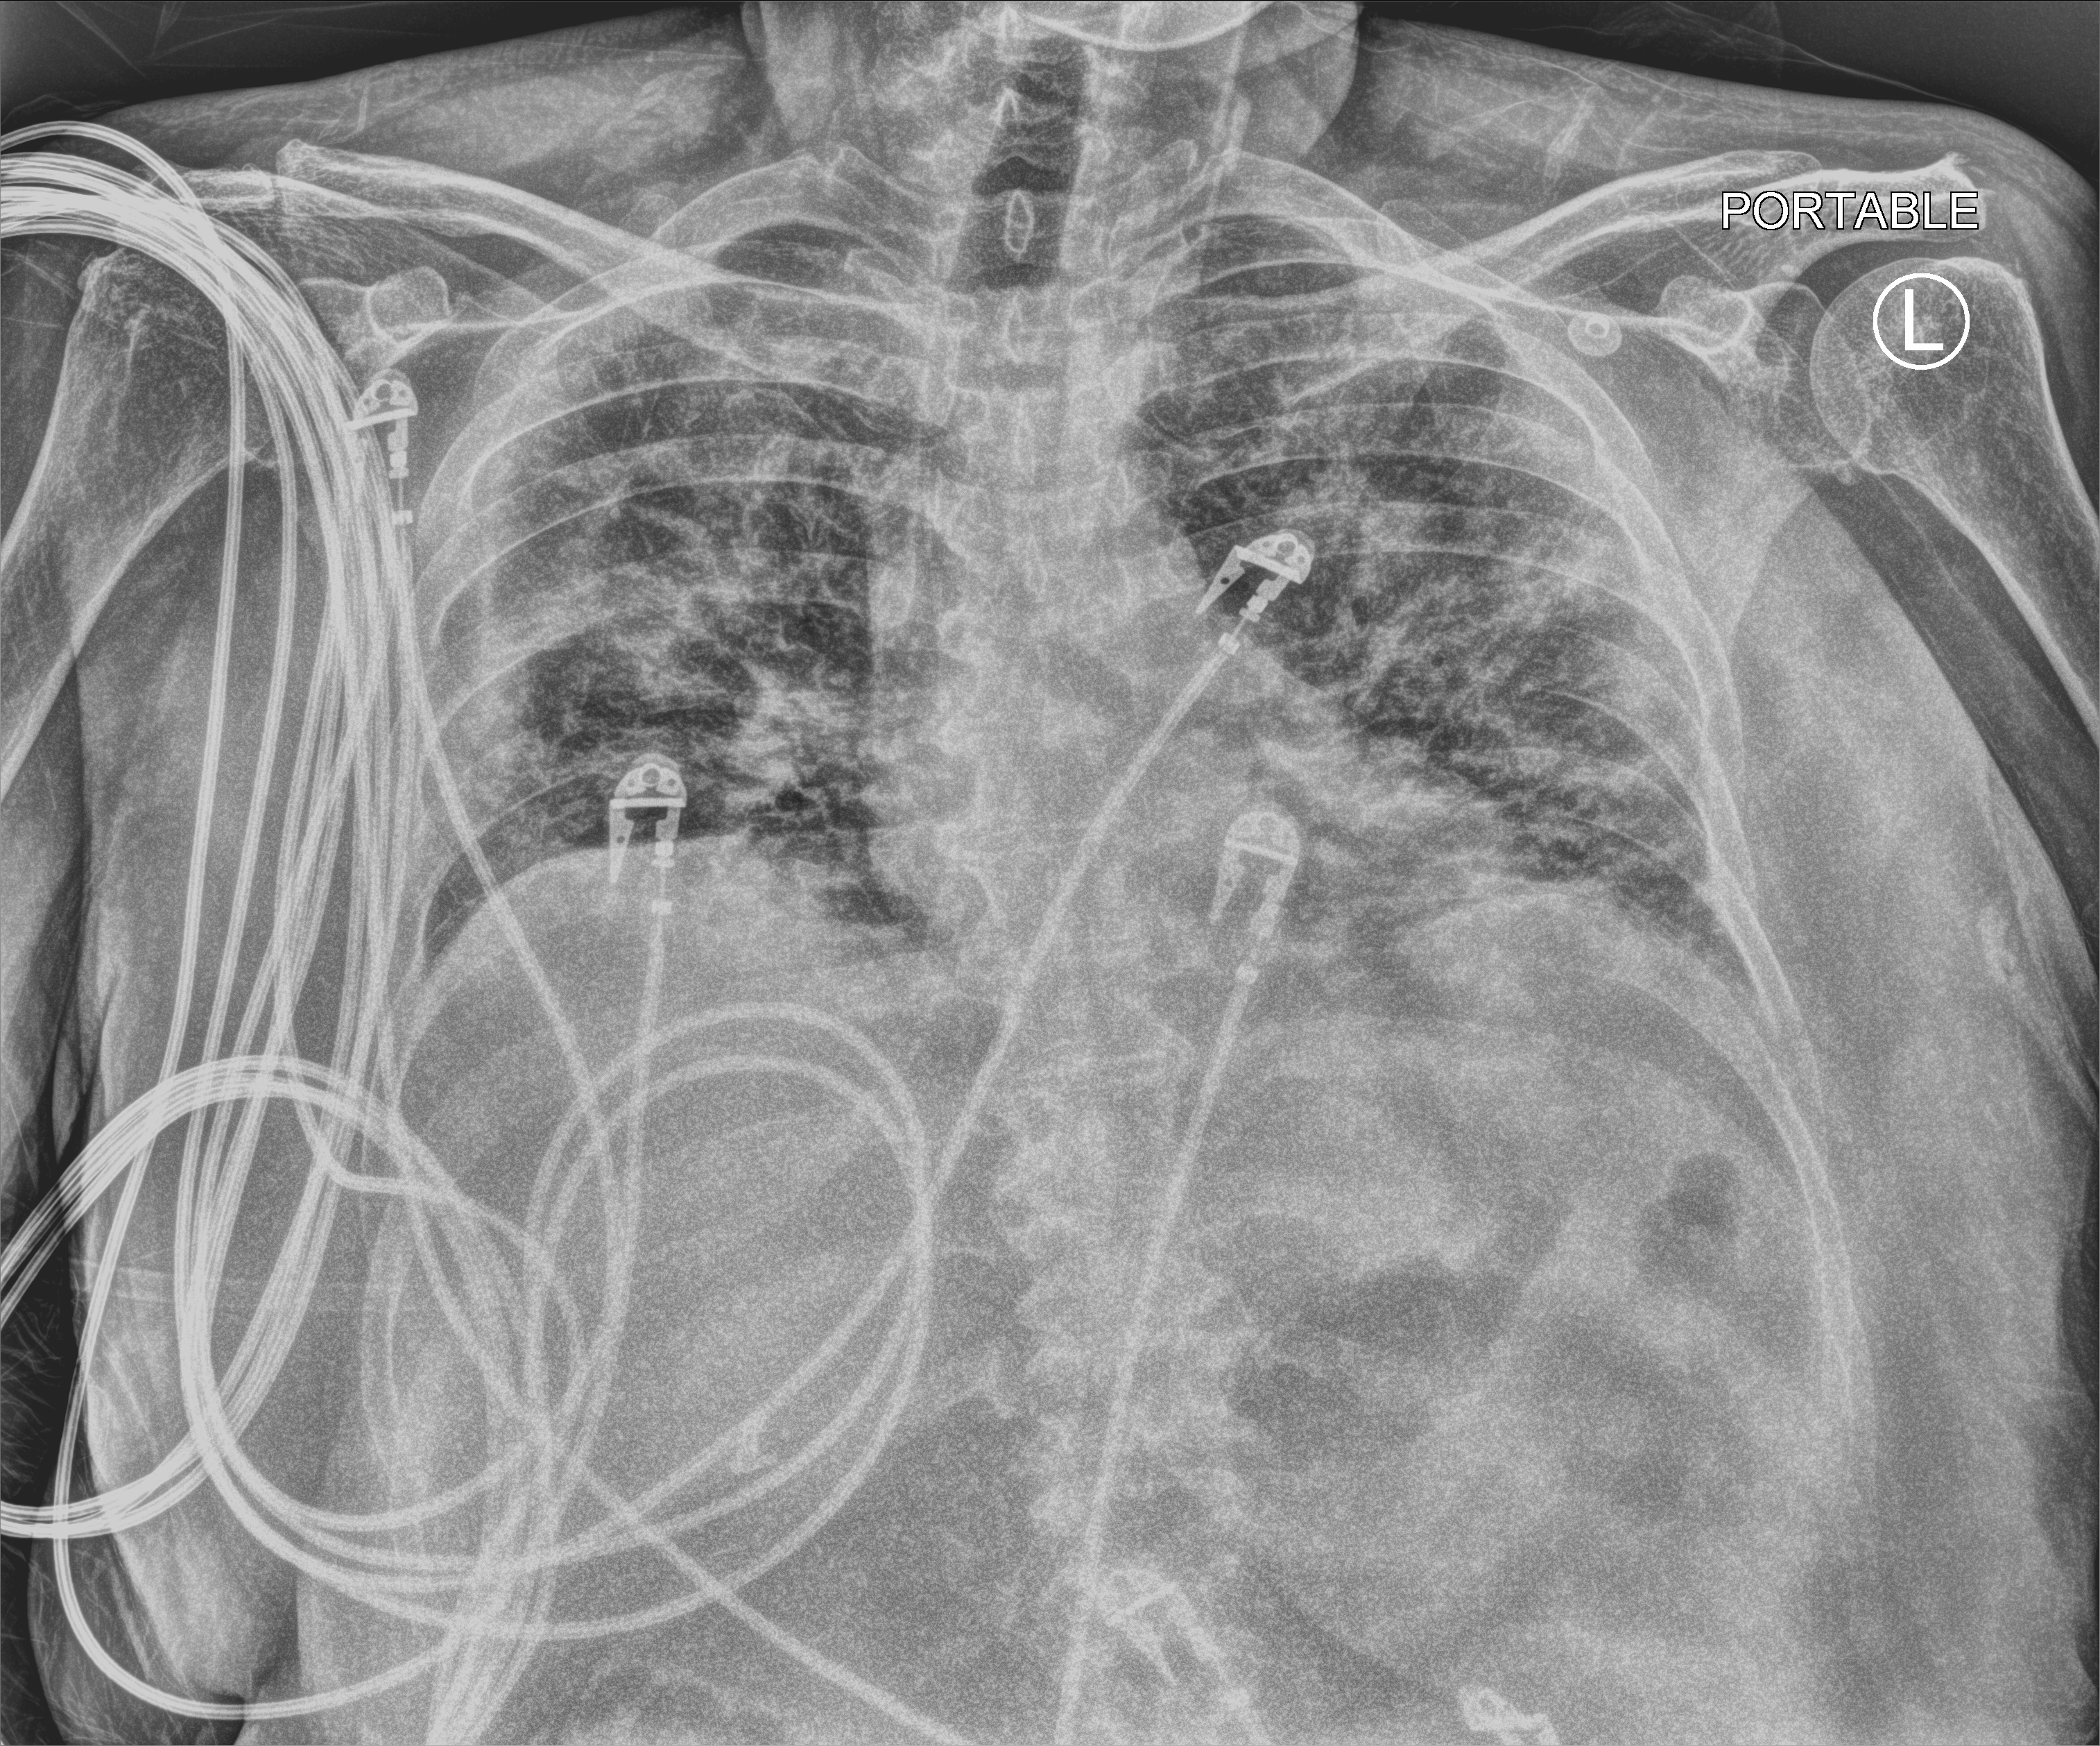
Portable chest radiograph, anteroposterior (AP) projection. Female patient hospitalised with COVID-19, age 18–59 years.
Admission-level facts for this patient (not findings on this image; timing relative to this image not recorded): chronic kidney disease (admission record): no.